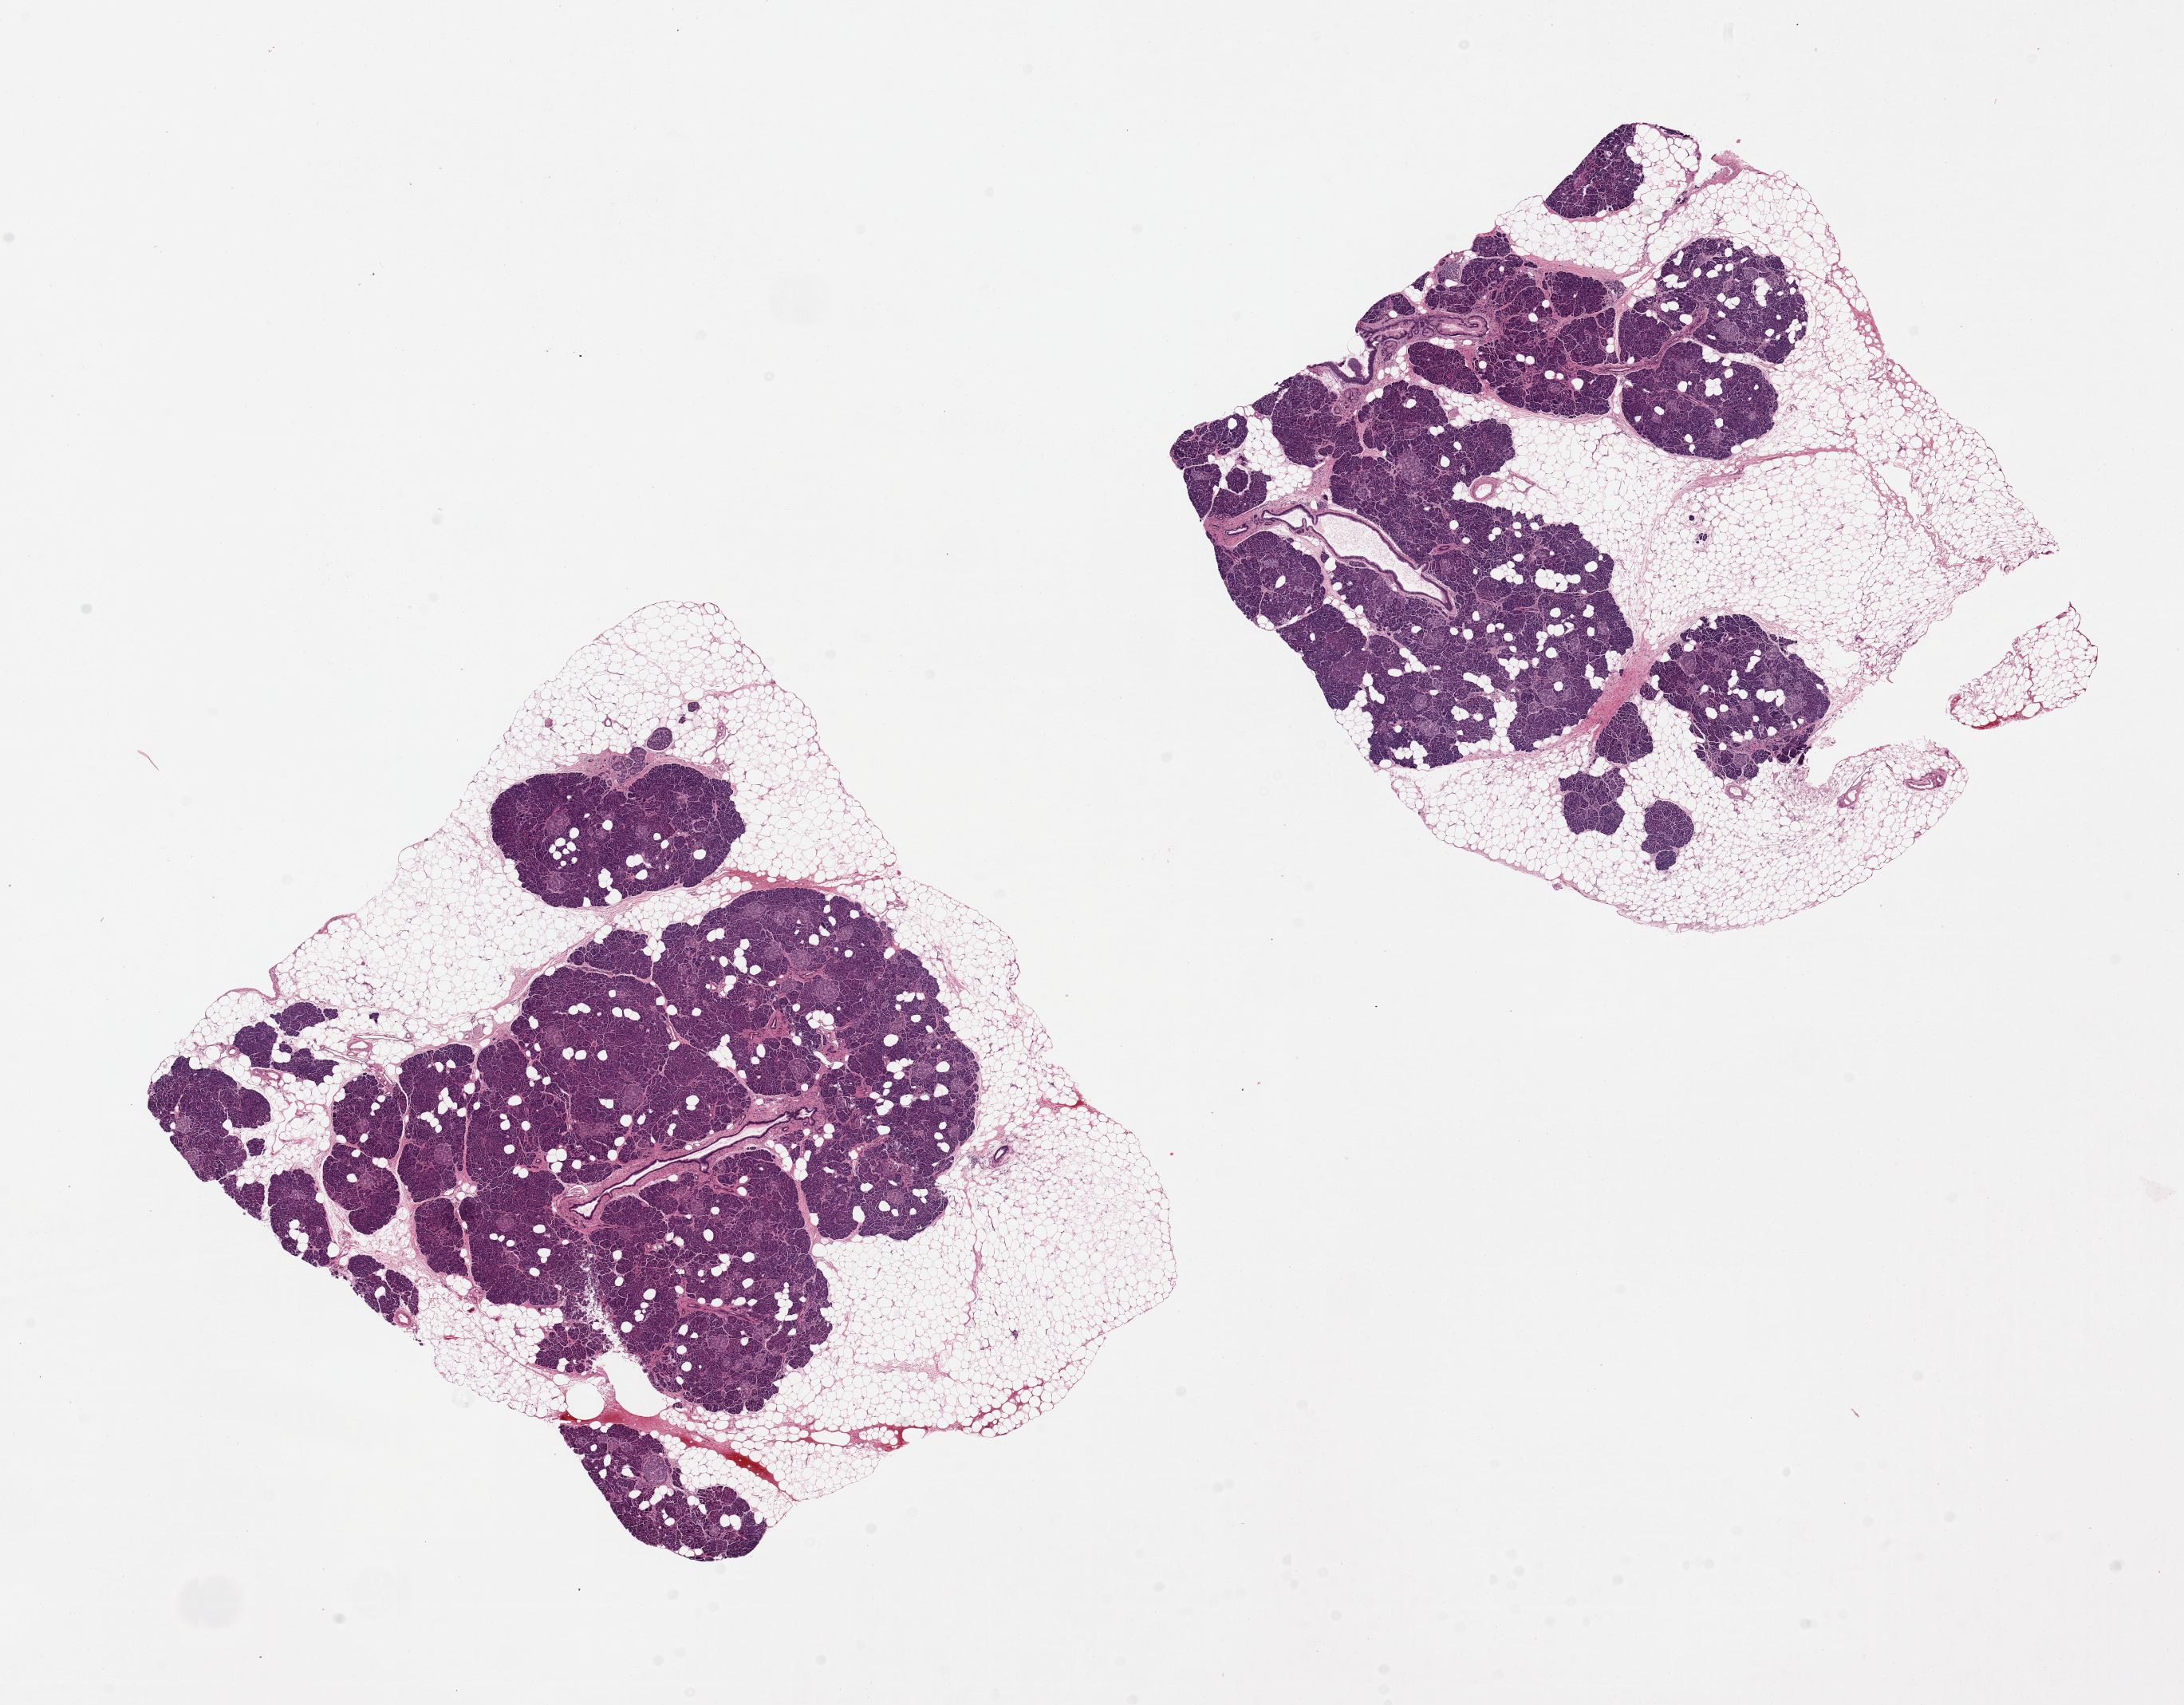
Hematoxylin and eosin (H&E) whole-slide image, brightfield — whole scanned area (about 21.7 x 16.9 mm, acquisition: 20x scan) shown as a low-resolution overview; PAXgene-fixed, paraffin-embedded tissue; sampled site (target tissue): pancreas; tissue donor sample. Male donor.
• reviewer comment on this tissue sample: 2 pieces, 9x8 & 8x7mm; 40-50% adipose, internal and external; 1 duct has mucinous metaplasia